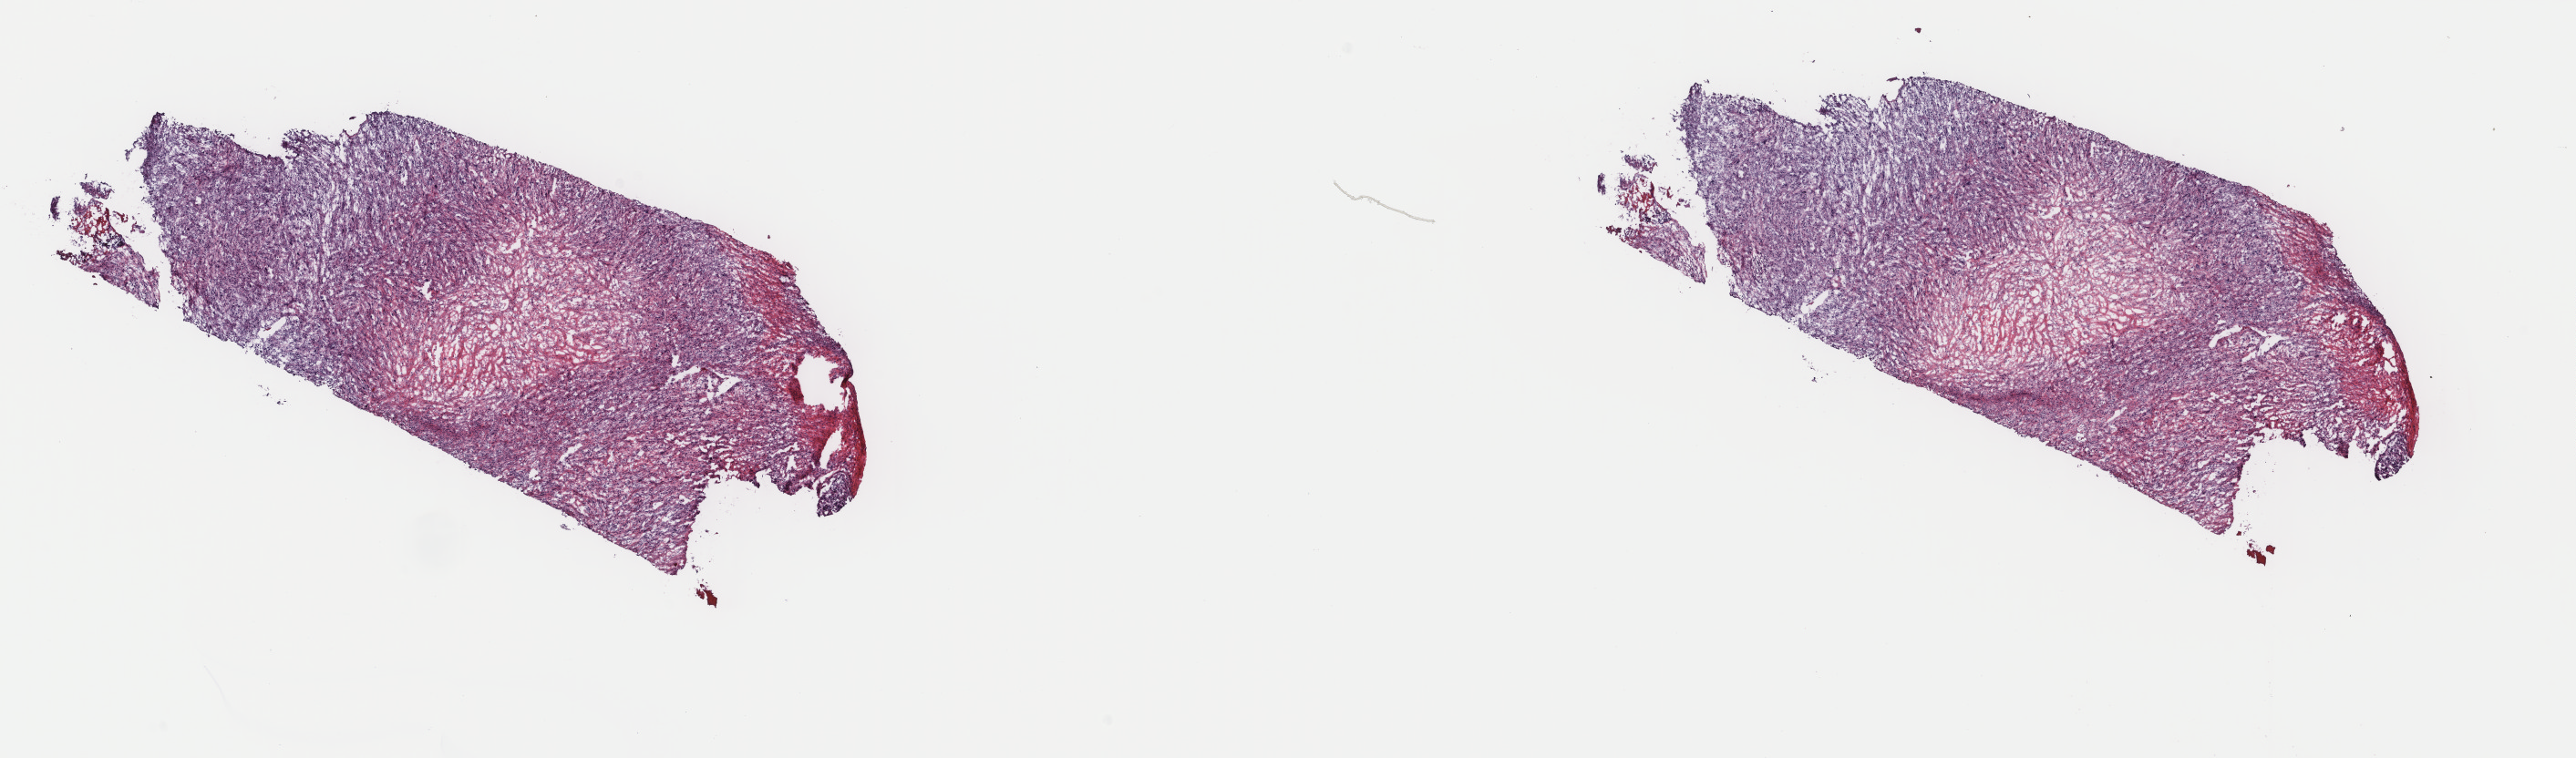
Whole-slide histology image, Hematoxylin and eosin (H&E) stained — whole scanned area (about 22.4 x 6.6 mm, acquisition: 40x scan) shown as a low-resolution overview, frozen section, connective, subcutaneous and other soft tissues, primary tumour sample. Patient: male, age at initial diagnosis 76 years. Composition of this section per pathologist review: tumour cells 97%, tumour nuclei 80%, normal cells 0%, stromal cells 0%, necrosis 3%. Inflammatory infiltration, as recorded: lymphocyte infiltration 1%, monocyte infiltration 0%, neutrophil infiltration 0%.
Diagnosis: Undifferentiated sarcoma.